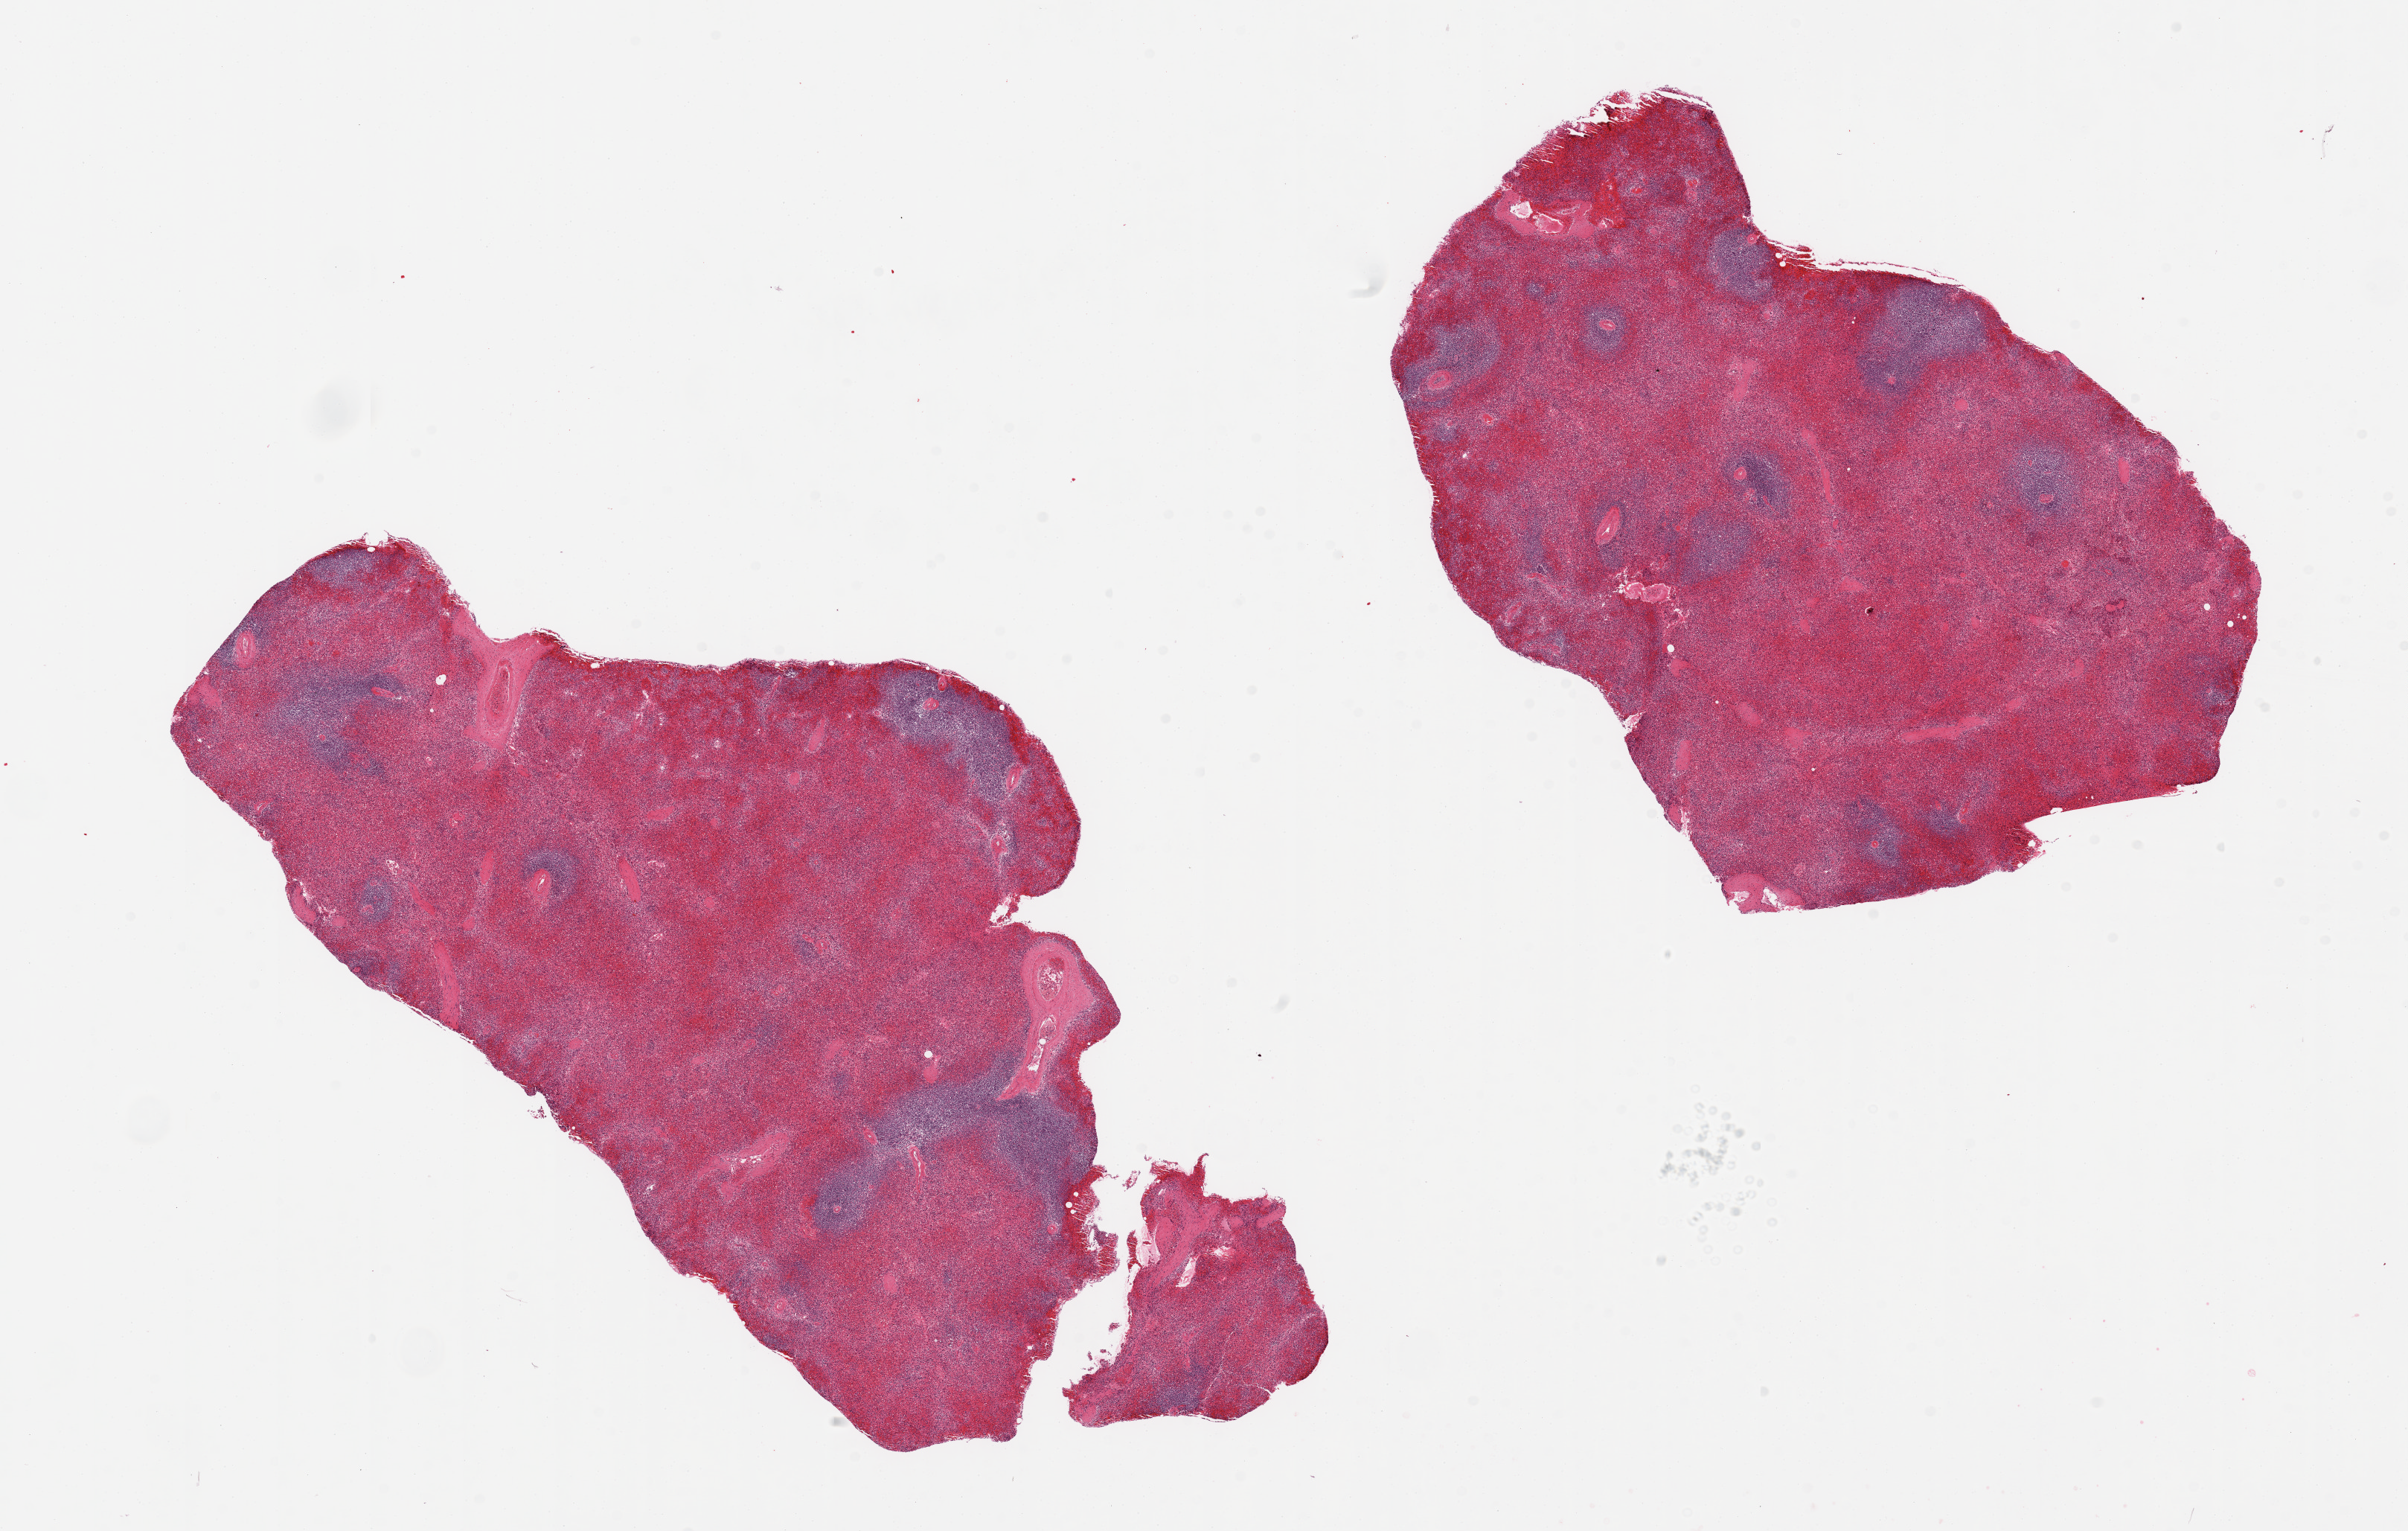
Digitized haematoxylin and eosin-stained section, brightfield — whole scanned area (about 25.6 x 16.3 mm, acquisition: 20x scan) shown as a low-resolution overview, PAXgene-fixed, paraffin-embedded tissue, target tissue: spleen, donor tissue sample. Donor: male.
Review note (as recorded): 2 pieces; moderate congestion.